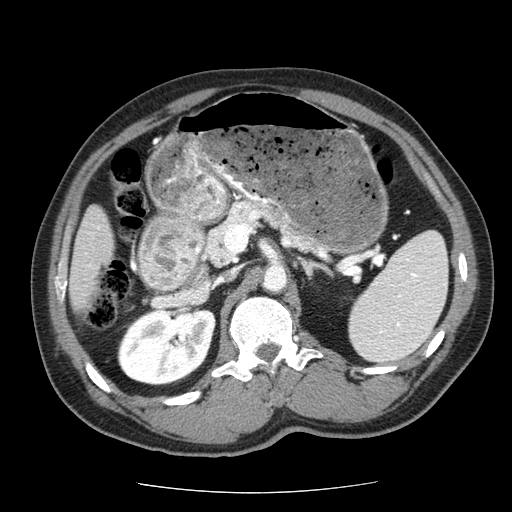
Contrast-enhanced abdominal CT (liver protocol), one axial slice; reconstruction kernel STANDARD; 120 kVp; soft-tissue window (W 400 / L 40 HU); 512 × 512 image matrix. From the clinical record (not read from this slice): diagnosis: hepatocellular carcinoma (patient treated with transarterial chemoembolisation; whether this scan precedes or follows treatment is not stated here); TNM stage (as recorded): Stage-IIIA; Child-Pugh class: A; tumour nodularity: multinodular; tumour size: 8 cm.
Outlined on this slice (semi-automatically segmented with operator editing):
- liver parenchyma outside the tumour (the mass and vessels are separate outlines, so this box may not span the whole liver): bounding box <70,205,112,311> (left, top, right, bottom; pixels)
- liver vessels: <88,227,99,267>